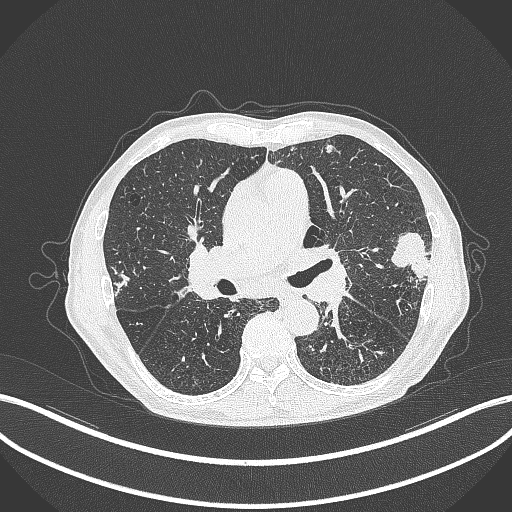
Chest CT, one axial slice. Position 231 of 463 along the scan axis. Reconstruction kernel B70f. 120 kVp. Lung window (W 1500 / L -600 HU). 1 mm slice thickness. 512 × 512 image matrix, field of view 400 × 400 mm. Patient: male, 74 years. Case-level facts recorded for this patient, not image findings: clinical TNM (as recorded): T2a N1 M0.
Annotated regions visible in this slice (bounding box drawn by a radiologist):
- lung tumour (recorded histology: adenocarcinoma): bounding box <387,227,433,282> (left, top, right, bottom; pixels)